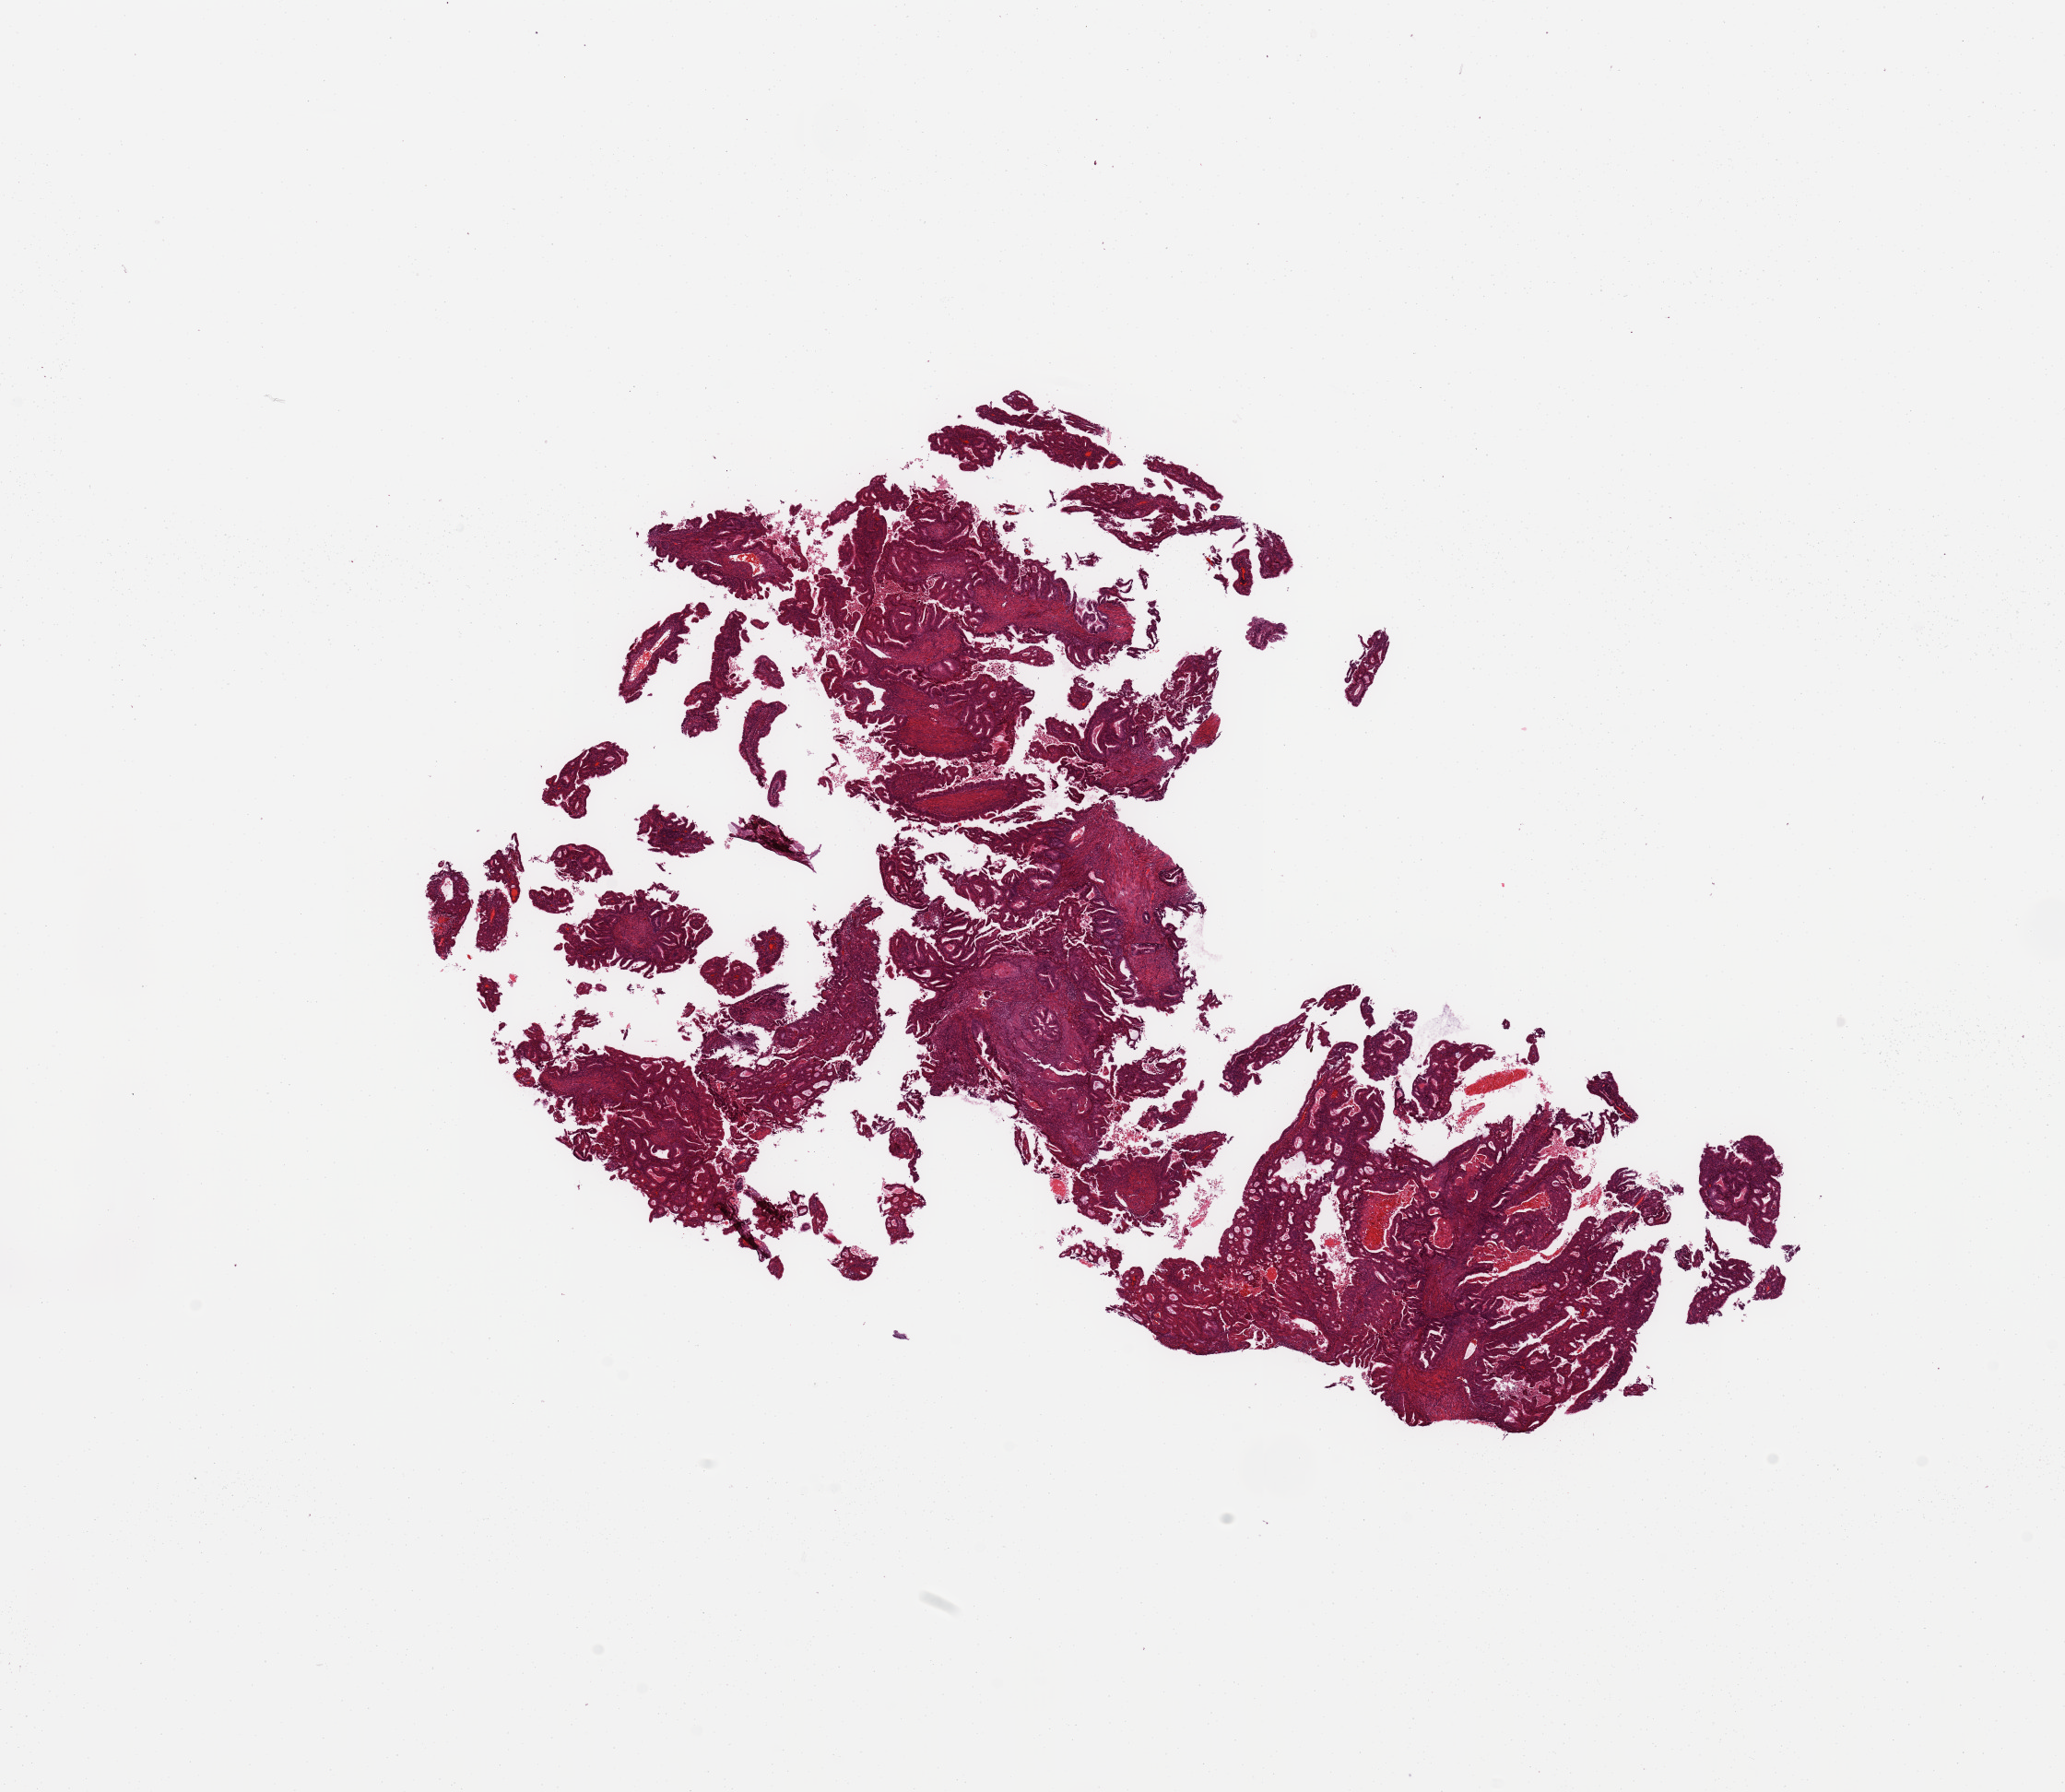
Hematoxylin and eosin (H&E) stained whole-slide image — whole scanned area (about 17.7 x 15.4 mm, slide scanned at 20x) shown as a low-resolution overview. Tumour tissue sample, sampled site: uterus. Patient: female, age 68 years. Histologic grade: G1 (well differentiated). Slide review estimates, as recorded: tumour nuclei 85%, necrosis 2%.
Diagnosis: Endometrioid adenocarcinoma, NOS. AJCC pathologic stage: IIIC1.